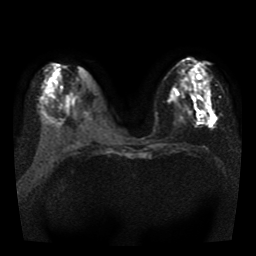
Breast MRI, one axial slice. Position 16 of 41 along the scan axis. Diffusion-weighted series; image 2 of 4 stored at this slice position (different b-values; order by instance number). 1.5 T. 256 × 256 image matrix, field of view 330 × 330 mm. Female patient.
Annotated regions visible in this slice (expert manual segmentation):
- tumour on diffusion-weighted imaging: bounding box <202,105,215,123> (left, top, right, bottom; pixels)